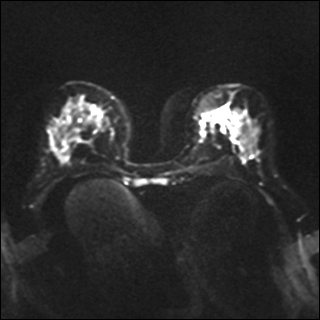
Breast MRI, one axial slice; slice 13 of 35 in the series (ordered by position); diffusion-weighted series; image 2 of 4 stored at this slice position (different b-values; order by instance number); 1.5 T; 4 mm slice thickness; 320 × 320 image matrix, field of view 320 × 320 mm. Female patient.
Annotated regions visible in this slice (outlined manually by an expert reader):
- tumour on diffusion-weighted imaging: bounding box [x1, y1, x2, y2] px = [212, 108, 227, 122]